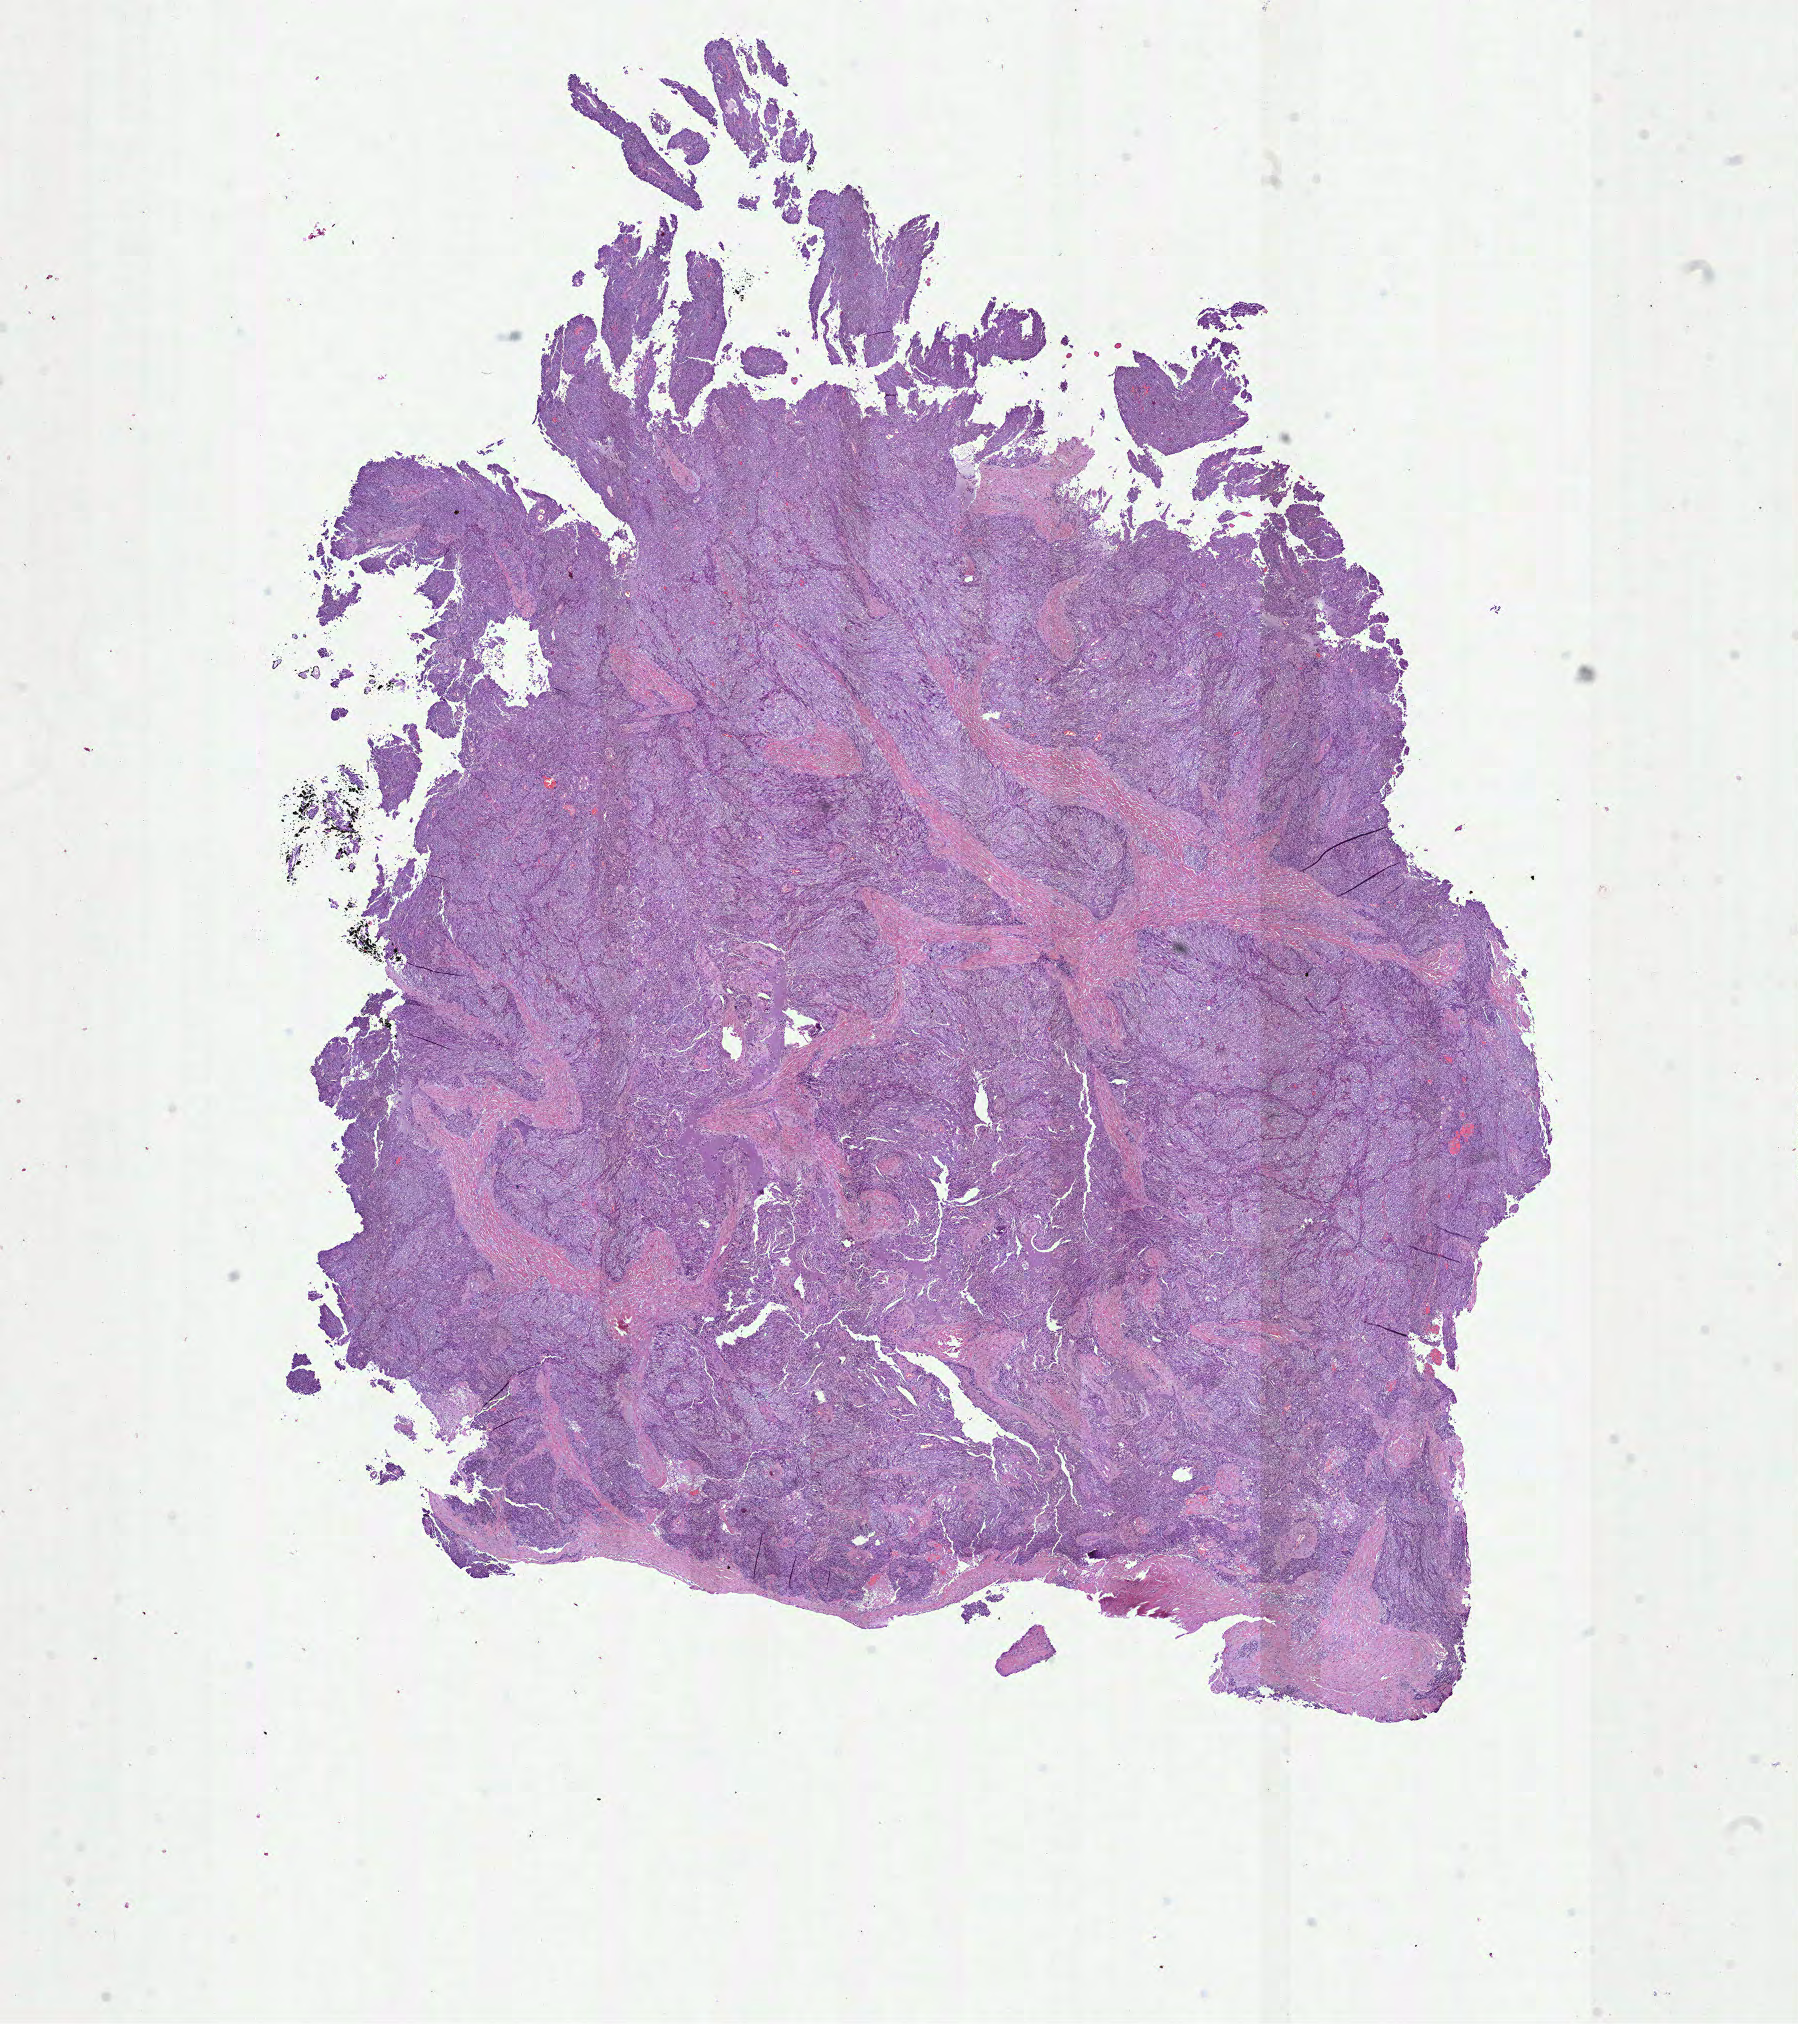
Hematoxylin and eosin (H&E) stained whole-slide image — a low-resolution overview of the entire scanned area, about 14.5 x 16.3 mm (slide scanned at 40x), formalin-fixed paraffin-embedded (FFPE) diagnostic section, sample: primary tumour, ovary. Female, age 57 years at initial diagnosis. Histologic grade: G3 (poorly differentiated).
Laterality: left. Histologic diagnosis: Serous cystadenocarcinoma, NOS. FIGO stage: IIIC.